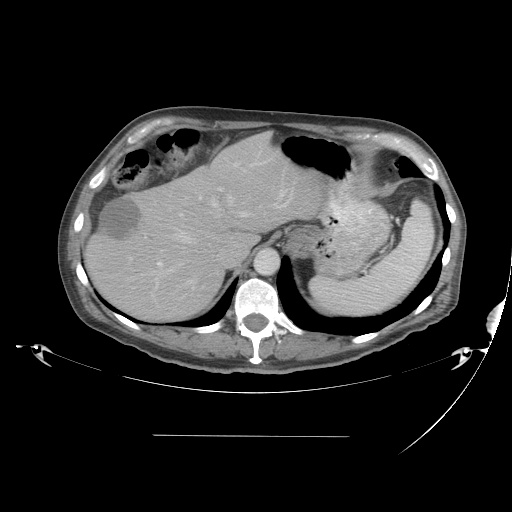
Contrast-enhanced abdominal CT, one axial slice; slice 32 of 48 in the series (ordered by position); soft-tissue window (W 400 / L 40 HU); 5 mm slice thickness; 512 × 512 image matrix. Male patient, age 65 years. From the clinical record (not read from this slice): diagnosis: colorectal cancer liver metastases, imaged before liver resection; multiple liver metastases: yes; largest metastasis: 11 cm; disease in both lobes: yes.
Annotated regions visible in this slice (expert manual segmentation):
- hepatic veins: box from (x=141, y=150) to (x=289, y=291) px
- liver: (x=87, y=135)–(x=318, y=322)
- planned liver remnant (the part of the liver to remain after resection): (x=169, y=135)–(x=318, y=246)
- portal vein (with intrahepatic branches): (x=157, y=162)–(x=250, y=267)
- liver metastasis: (x=97, y=198)–(x=141, y=239)